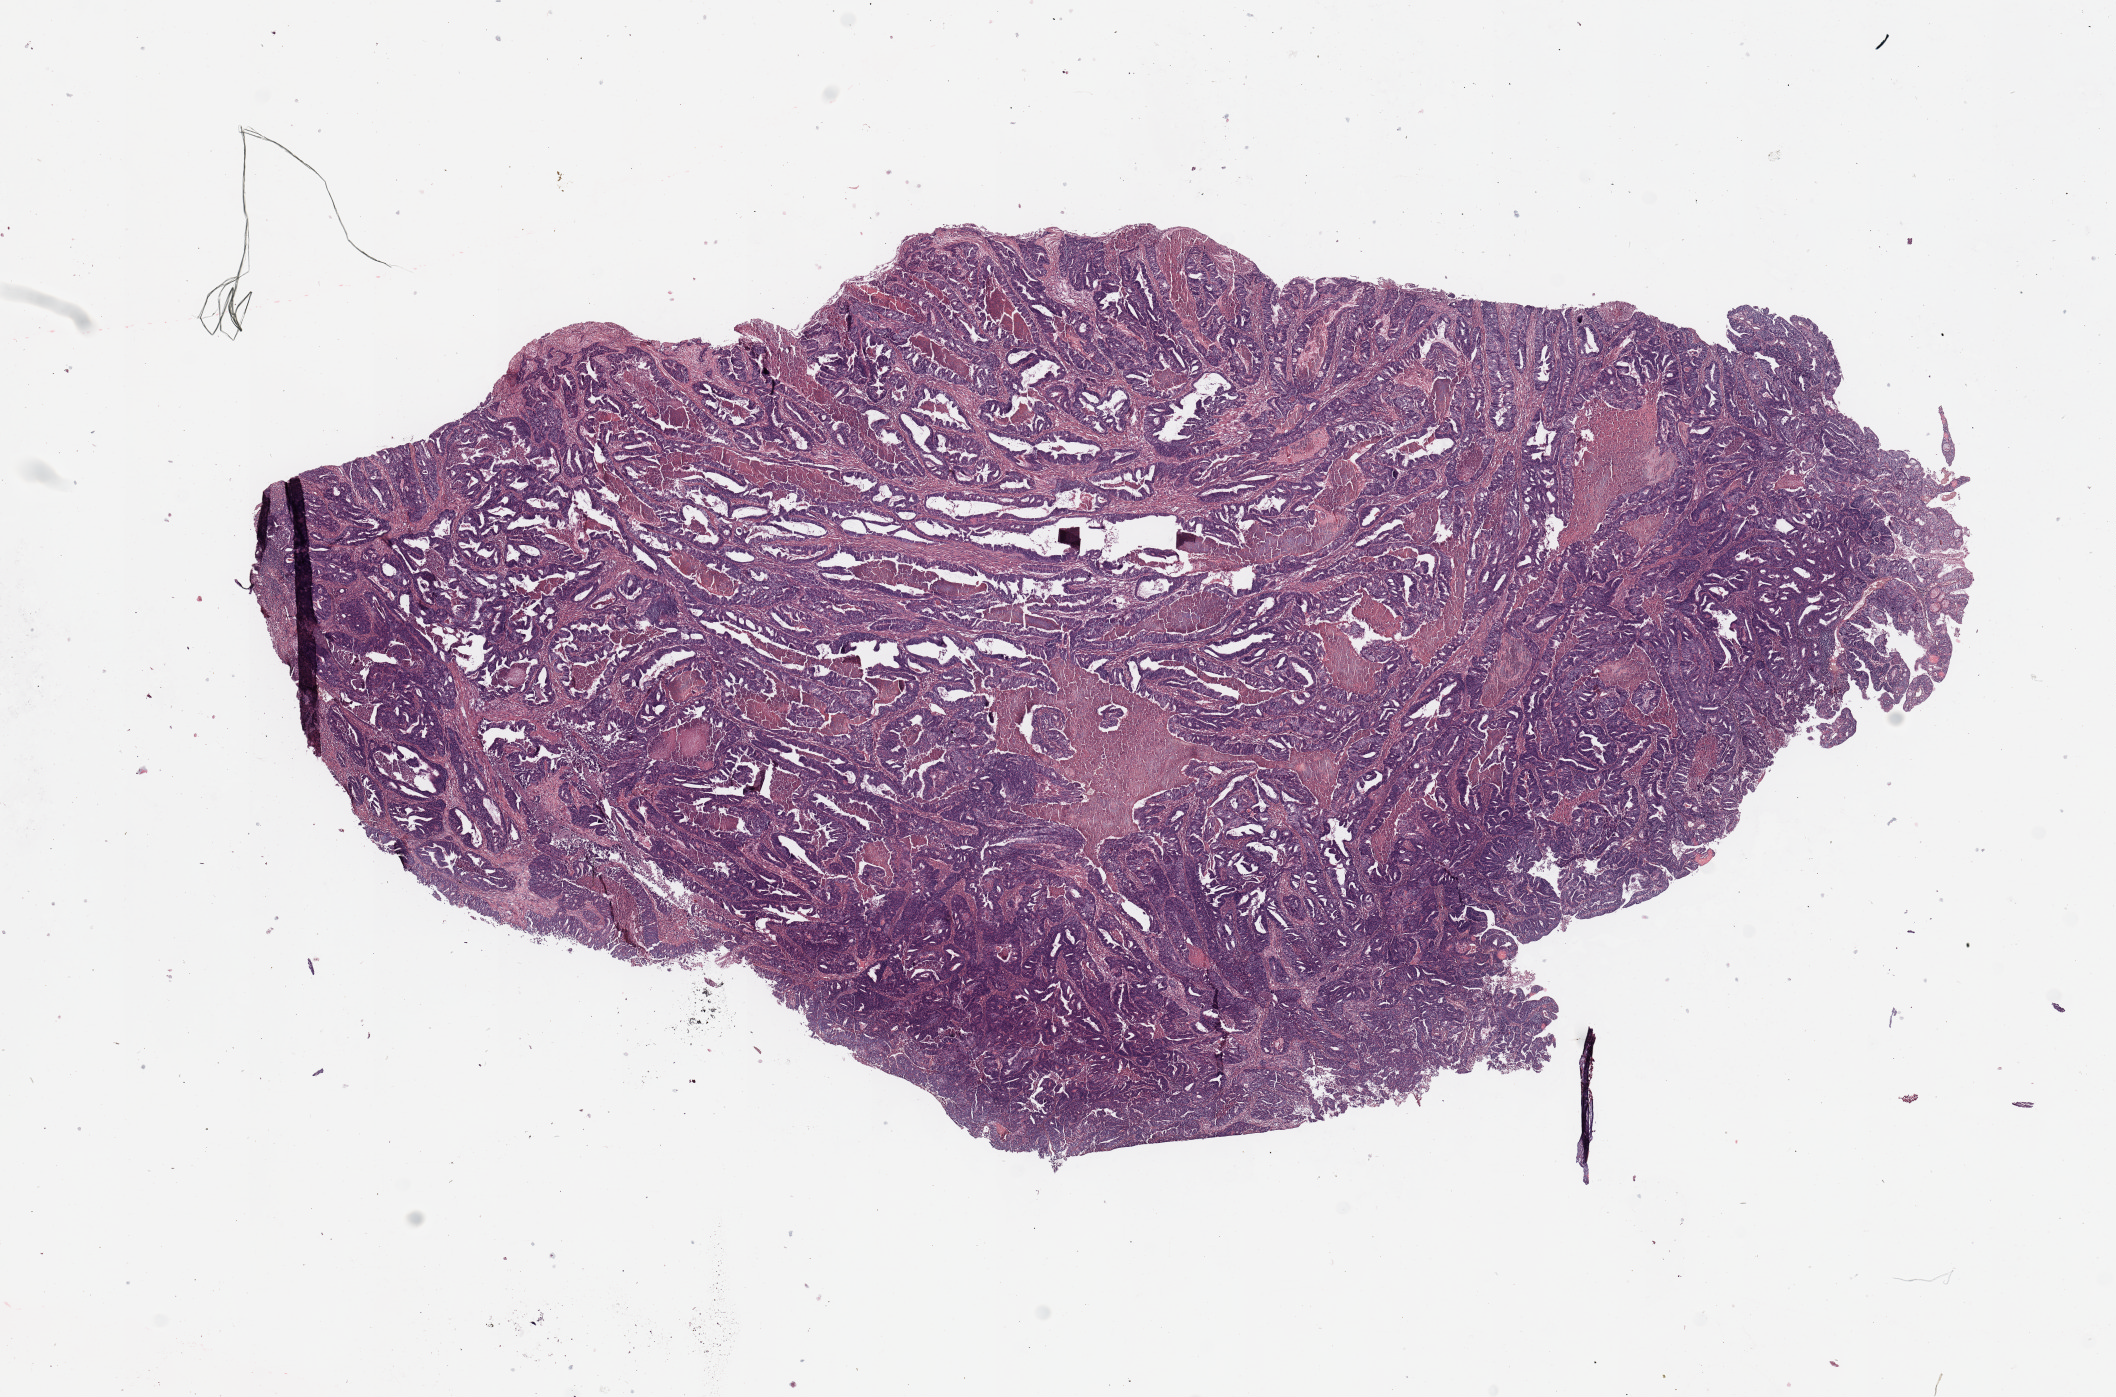
Digitized Hematoxylin and eosin (H&E) stained tissue section (whole slide), a low-resolution overview of the entire scanned area, about 16.7 x 11.0 mm; tumour tissue sample, sampled site: uterus. Patient: female, age 62 years. Histologic grade: G2 (moderately differentiated). Pathologist review of this section (percent, as recorded): tumour nuclei 90%, necrosis 5%.
* diagnosis: Endometrioid adenocarcinoma, NOS
* AJCC pathologic stage: I